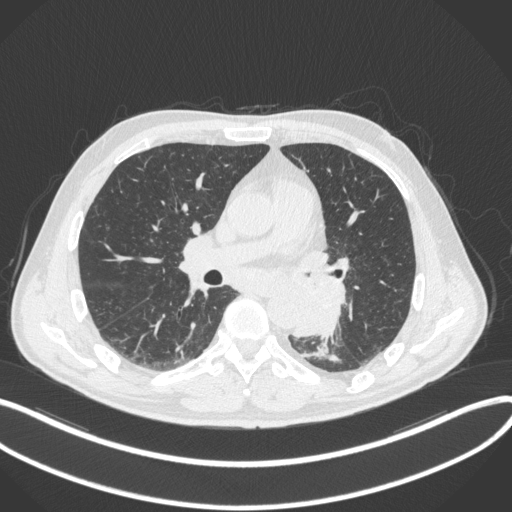
Chest CT, one axial slice. Position 181 of 328 along the scan axis. 120 kVp. Lung window (W 1500 / L -600 HU). 512 × 512 image matrix, field of view 400 × 400 mm. Male patient, age 59 years. From the clinical record (not read from this slice): clinical TNM (as recorded): T2a N2 M0.
Outlined on this slice (bounding box drawn by a radiologist):
- lung tumour (recorded histology: squamous cell carcinoma): bounding box <288,272,350,341> (left, top, right, bottom; pixels)